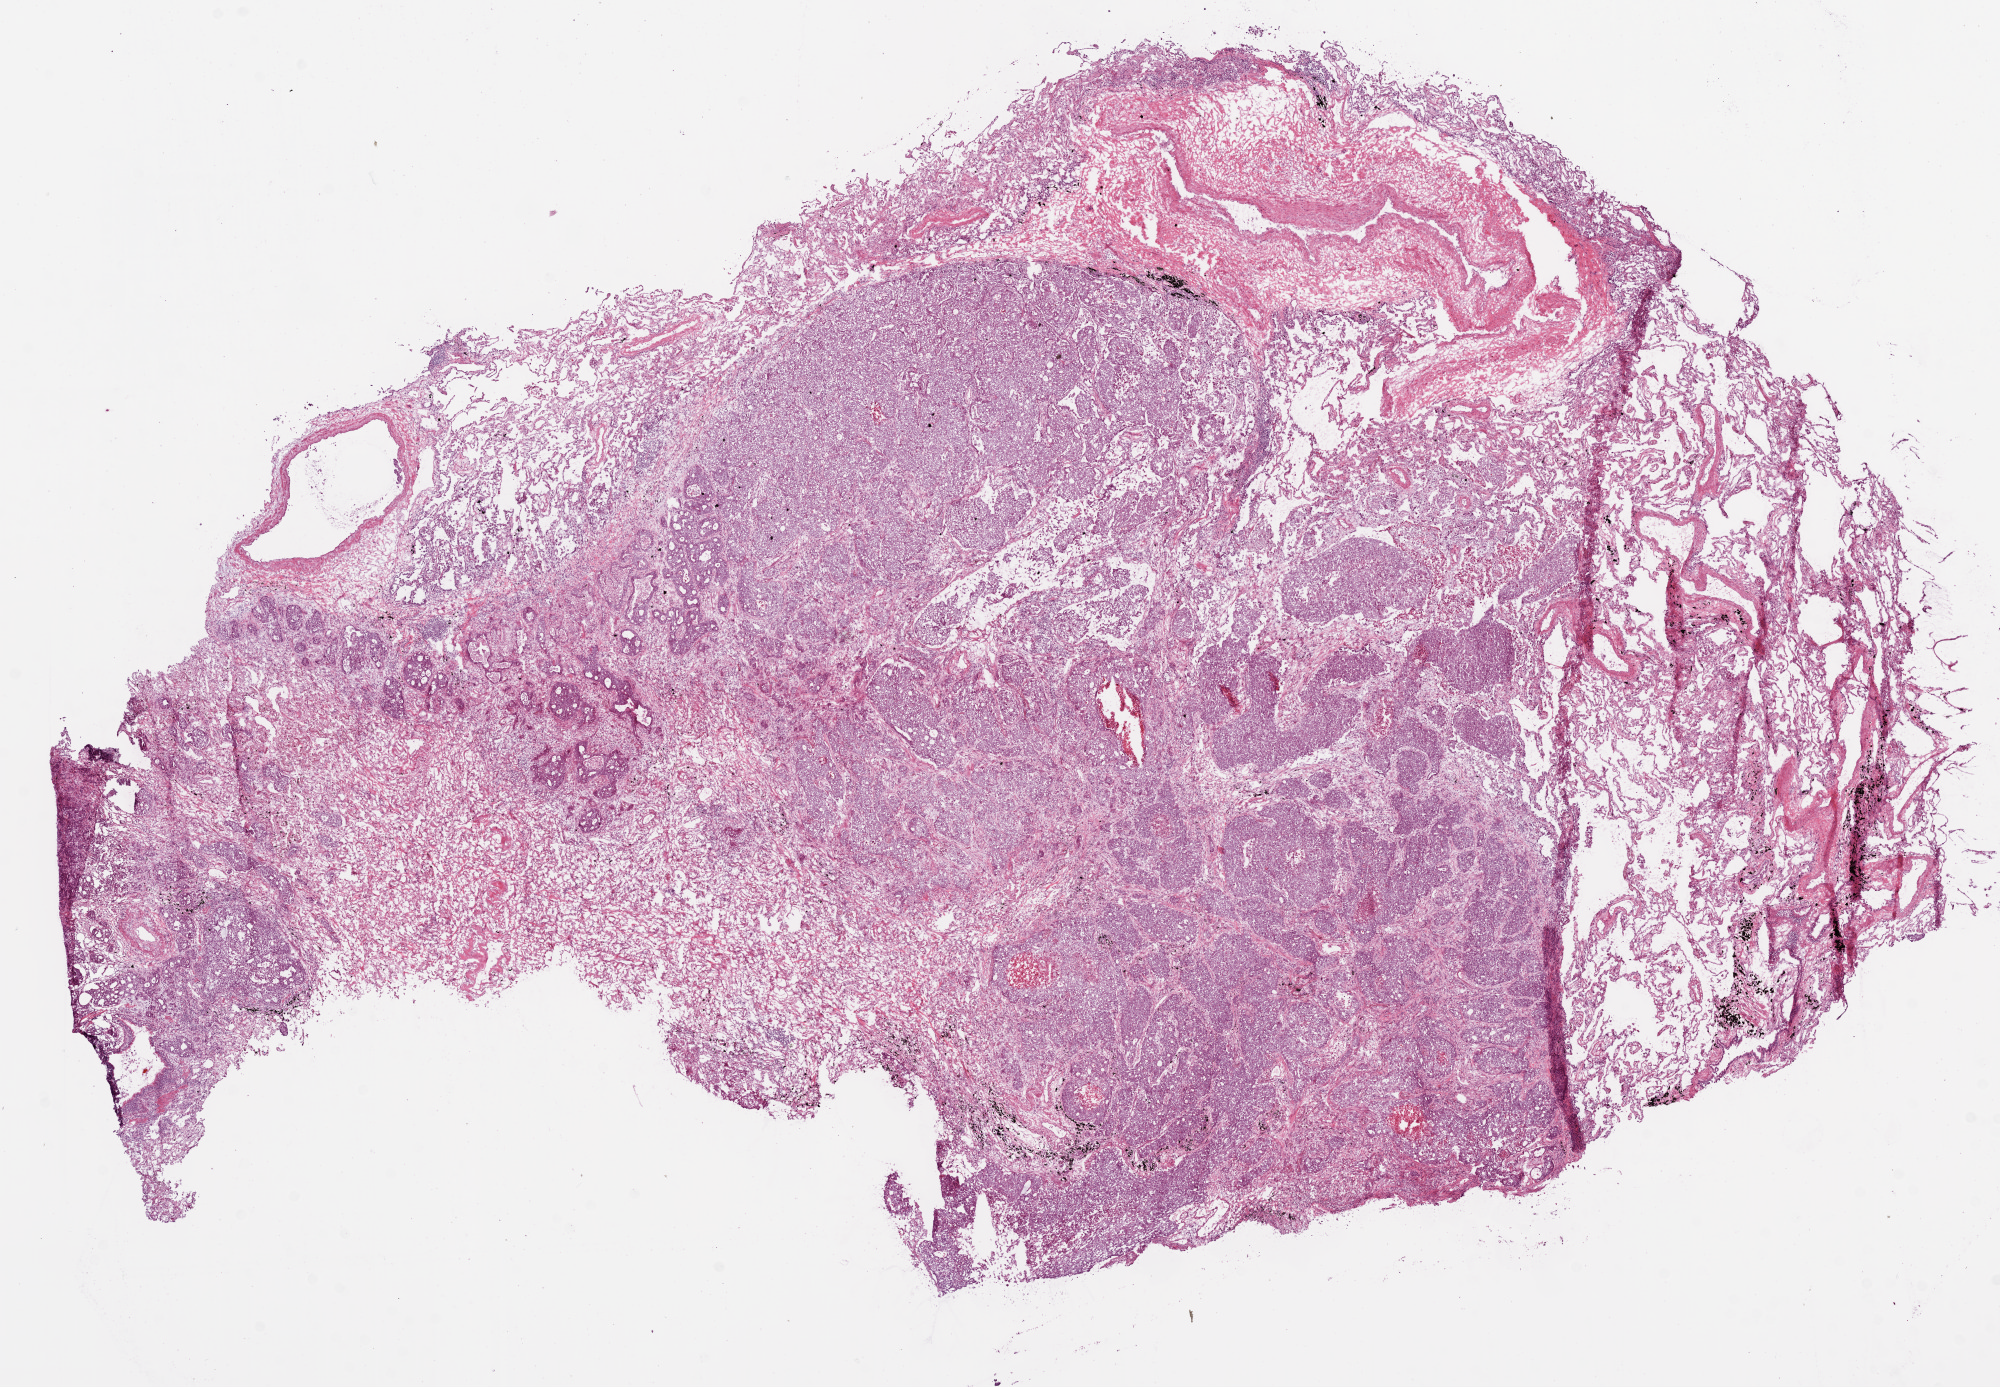
H&E-stained whole-slide image — whole scanned area (about 16.0 x 11.1 mm, from a 20x scan) shown as a low-resolution overview, frozen section, sample: primary tumour, lung. Male patient; age at initial diagnosis 74 years. Pathologist review of this section (percent, as recorded): tumour cells 55%, tumour nuclei 70%, normal cells 20%, stromal cells 20%, necrosis 5%.
Pathologic diagnosis: Adenocarcinoma, NOS (upper lobe, lung). TNM: T2 N2 M0. AJCC pathologic stage: IIIA.